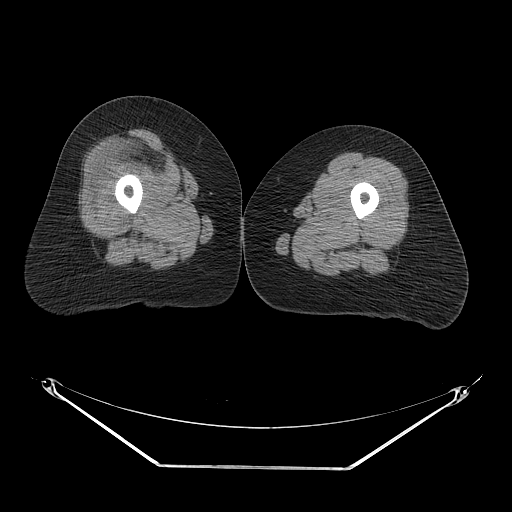
CT of an extremity soft-tissue mass (from a PET/CT study), one axial slice. Slice 21 of 267 in the series (ordered by position). 140 kVp. Soft-tissue window (W 400 / L 40 HU). 3.75 mm slice thickness. 512 × 512 image matrix. Female patient. Case-level facts recorded for this patient, not image findings: histological type: malignant solitary fibrous tumor; grade: intermediate; site of the primary tumour: right thigh.
Annotated regions visible in this slice (expert contour drawn on MRI and transferred to this co-registered scan by the dataset authors):
- gross tumour volume including surrounding oedema: bounding box (x1, y1, x2, y2) in pixels: (119, 130, 195, 179)